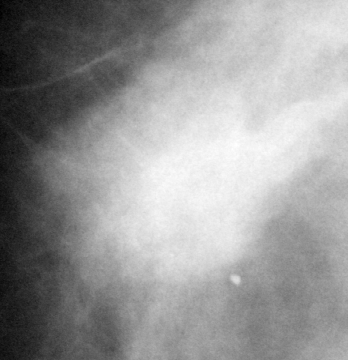
Crop from a digitized film mammogram around one marked abnormality, right breast, MLO view, BI-RADS breast density category 2 (scale 1–4).
- Mass, shape irregular, margins microlobulated; BI-RADS assessment category 5; subtlety rating 5 on a 1 (subtle) to 5 (obvious) scale; pathology (as recorded): malignant.